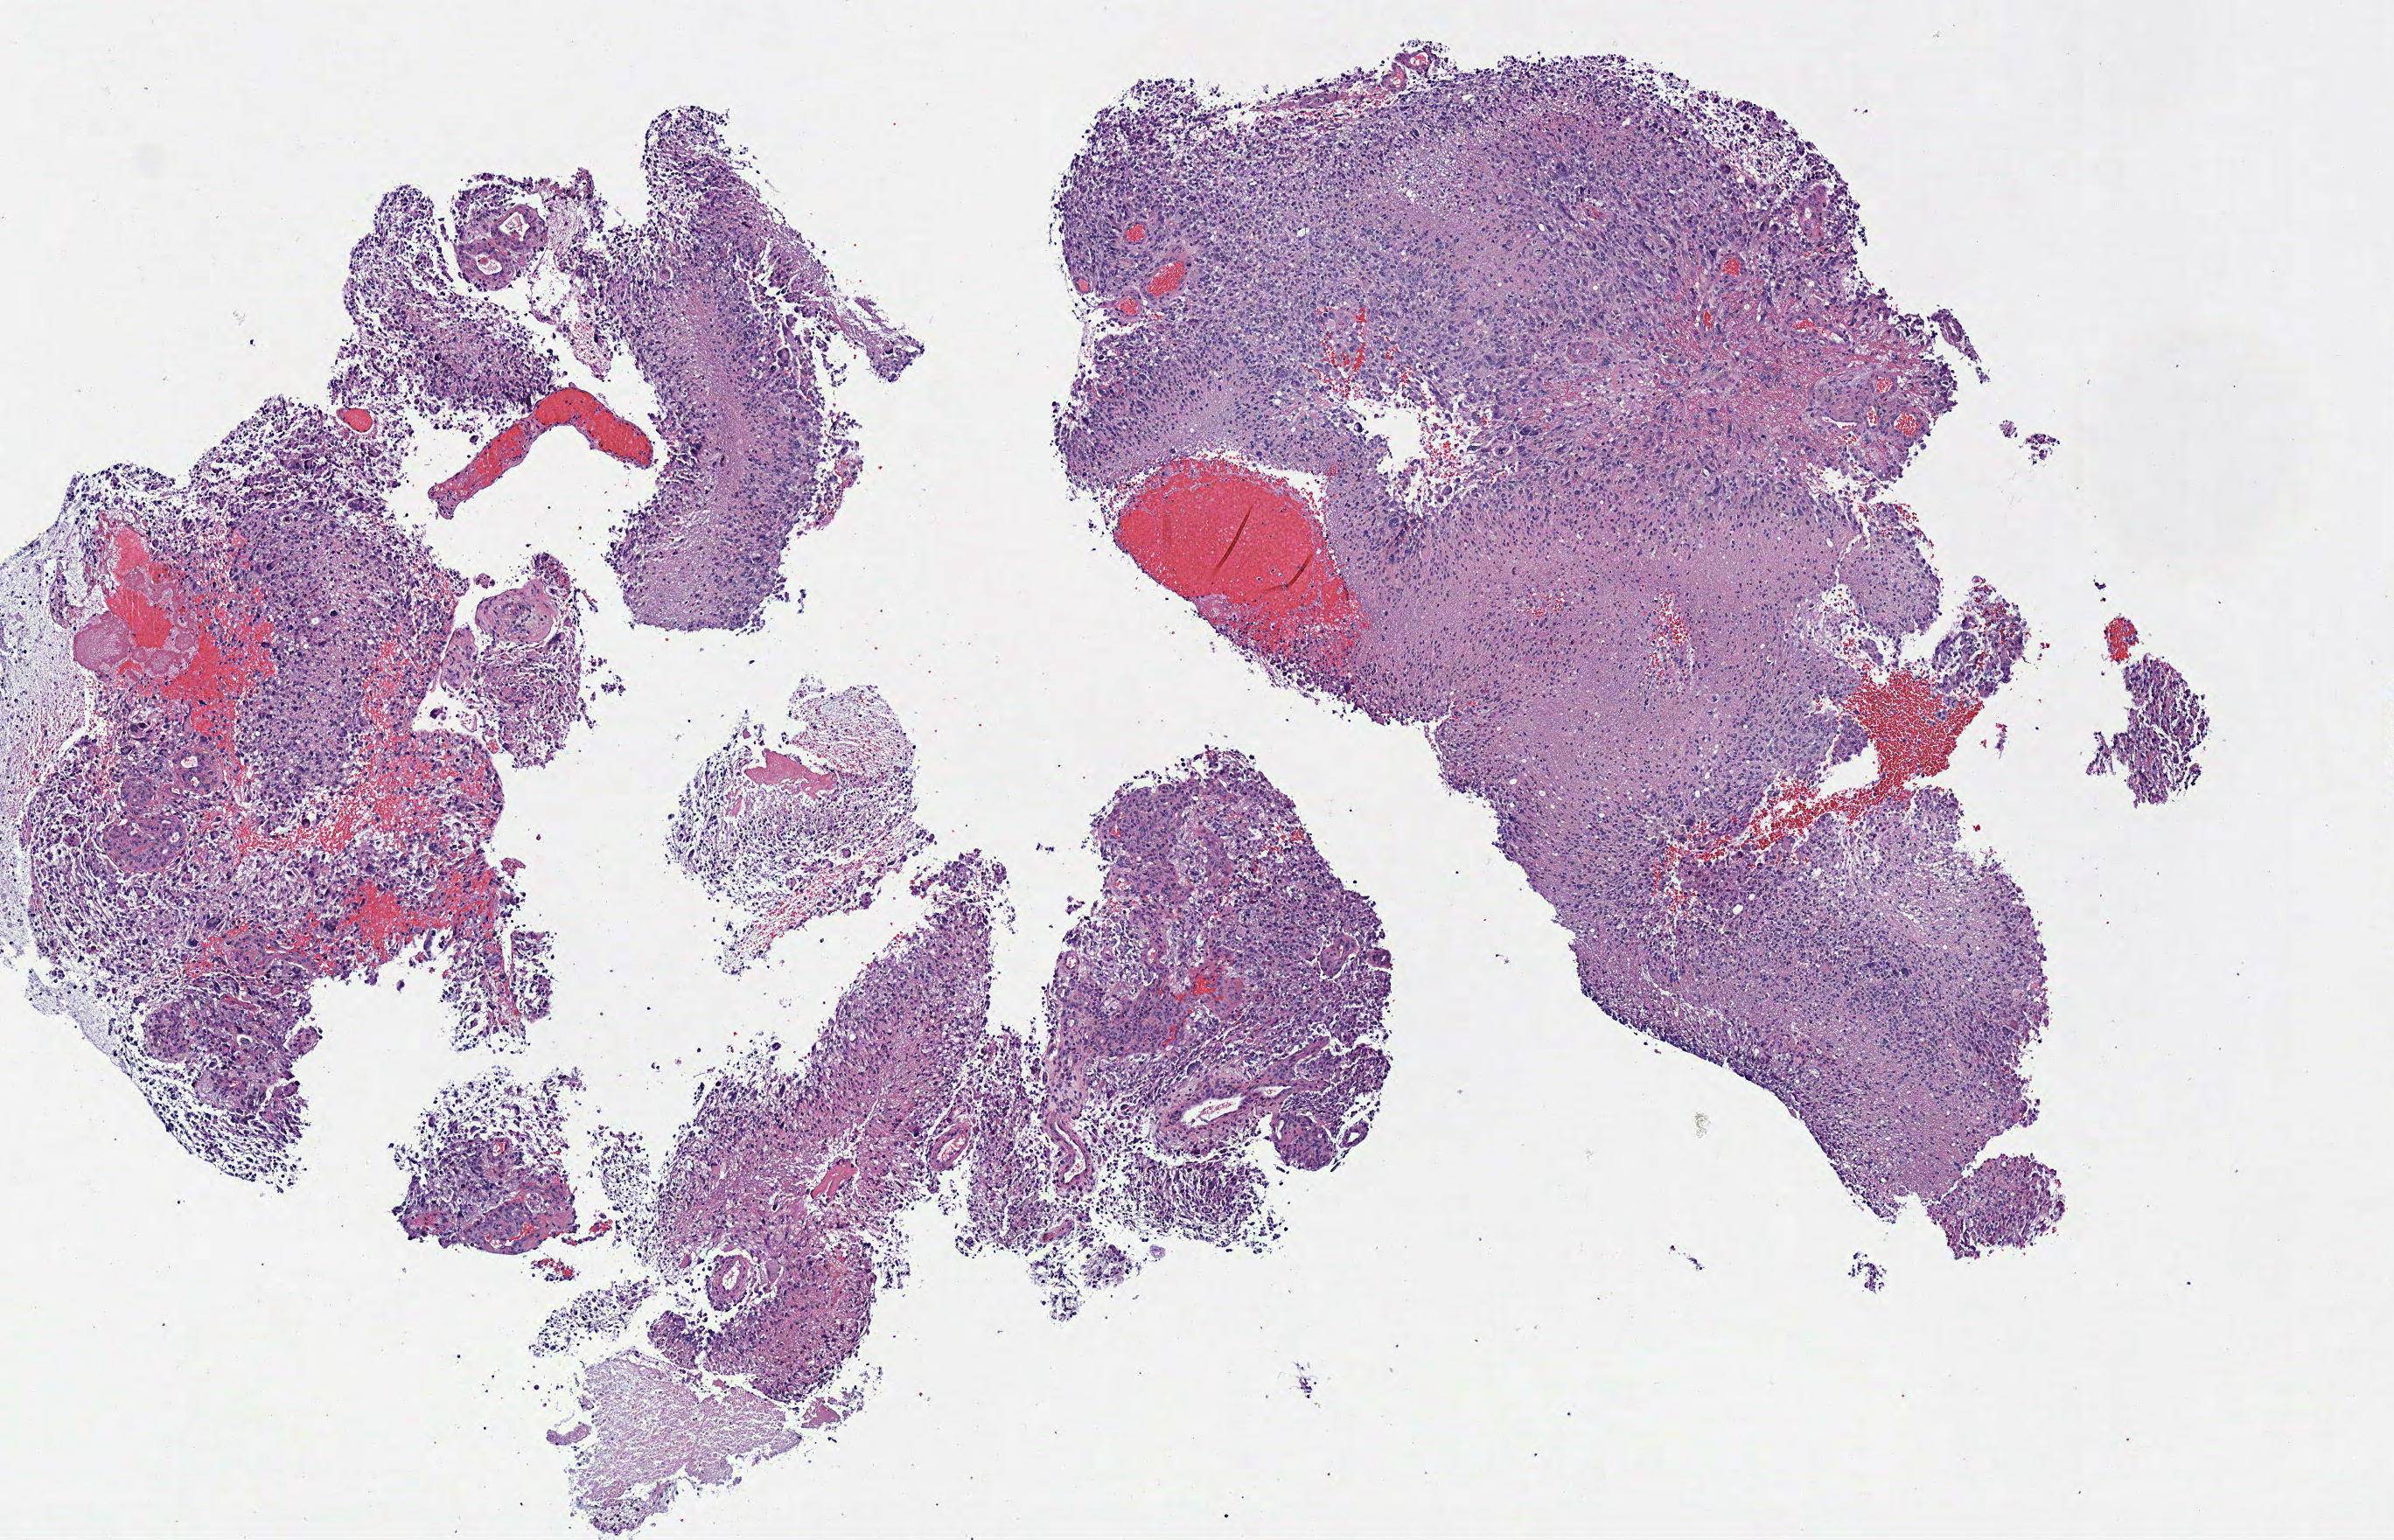
Whole-slide histology image, H&E, whole scanned area (about 5.4 x 3.5 mm, slide scanned at 40x) shown as a low-resolution overview, frozen section from the top of the tissue portion, primary tumour sample from the brain. Female, age 45 years at initial diagnosis. Slide review estimates, as recorded: tumour cells 82%, tumour nuclei 85%, normal cells 0%, stromal cells 0%, necrosis 18%.
• diagnosis: Glioblastoma